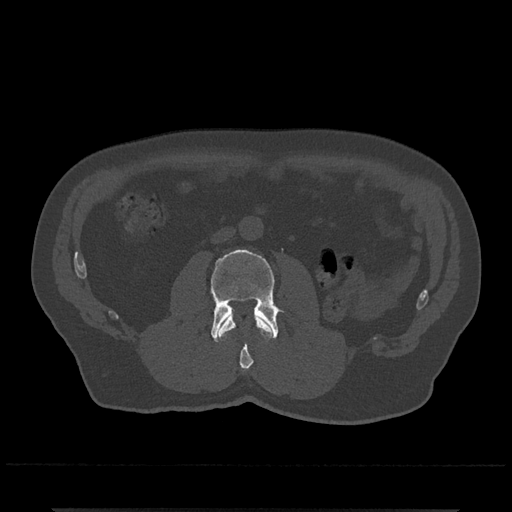
CT including the spine, one axial slice. Position 244 of 797 along the scan axis. Reconstruction kernel Br40s/3. Bone window (W 1800 / L 400 HU). 0.5 mm slice thickness. 512 × 512 image matrix, field of view 393 × 393 mm. Patient: male, 67 years. Case-level facts recorded for this patient, not image findings: primary cancer: prostate.
Annotated regions visible in this slice (semi-automatically segmented with operator editing):
- L2 vertebra: bounding box <219,315,272,370> (left, top, right, bottom; pixels)
- L3 vertebra: <210,249,280,342>